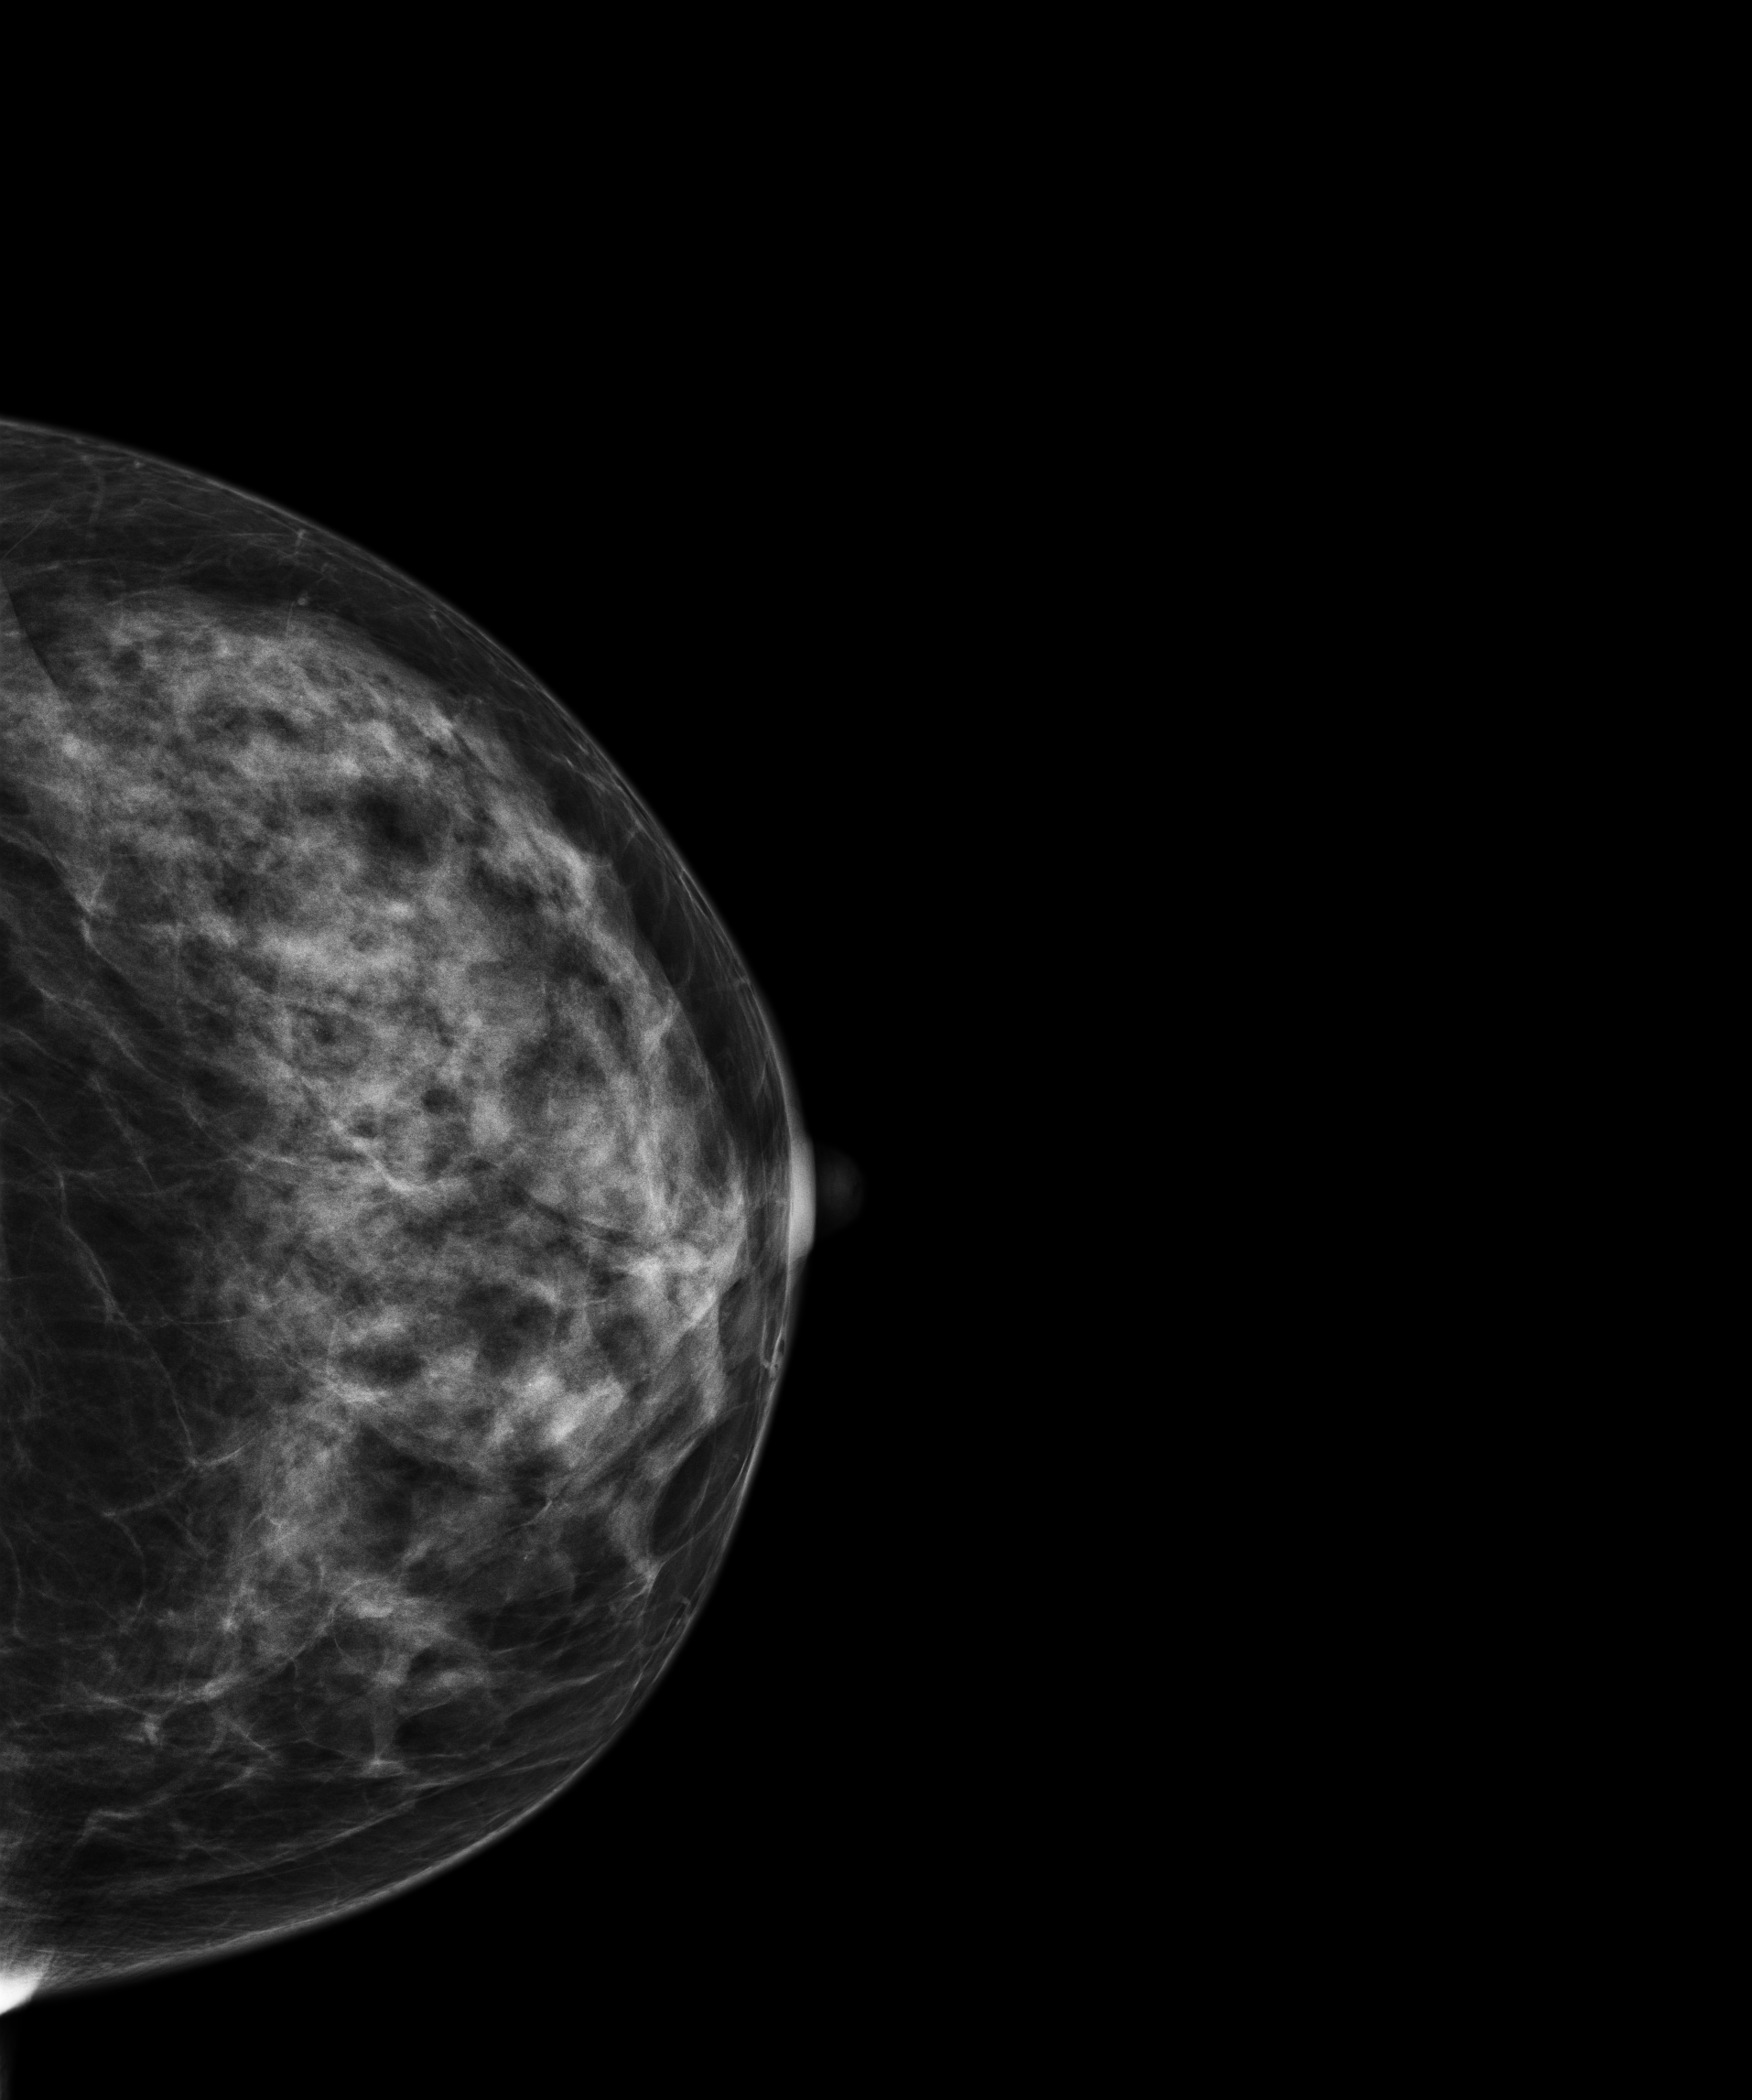
Full-field digital mammogram (FFDM); left breast; craniocaudal (CC) view; annual screening mammography examination; compressed breast thickness 49 mm. Patient aged 58 years (female).
BI-RADS breast density category at the screening exam (both breasts, scale 1–4): 3. Final BI-RADS category for the screening round (tomosynthesis exam, both breasts): category 1. Recall: no recall after this screen.